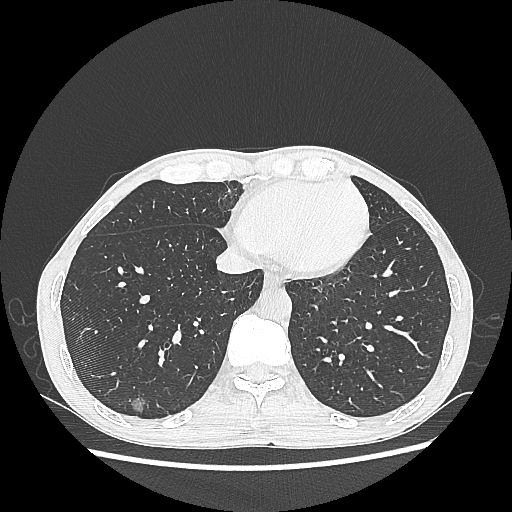
Chest CT, one axial slice. Slice 80 of 270 in the series (ordered by position). 100 kVp. Lung window (W 1500 / L -600 HU). 1.25 mm slice thickness. 512 × 512 image matrix, field of view 360 × 360 mm. Male patient, age 60 years. From the clinical record (not read from this slice): clinical TNM (as recorded): T1c N0 M0.
Annotated regions visible in this slice (bounding box drawn by a radiologist):
- lung tumour (recorded histology: adenocarcinoma): bounding box [x1, y1, x2, y2] px = [125, 392, 156, 421]